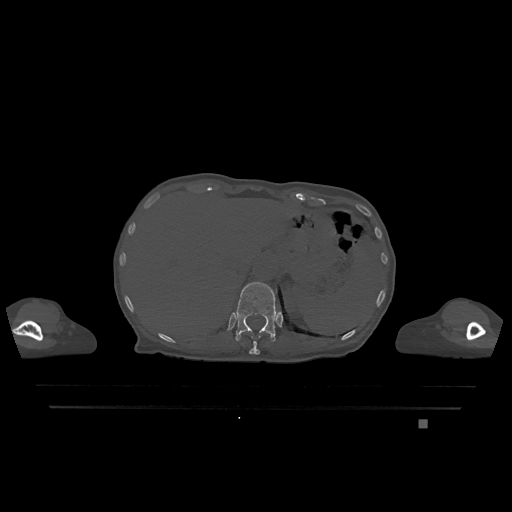
CT including the spine, one axial slice; slice 548 of 1317 in the series (ordered by position); bone window (W 1800 / L 400 HU); 0.5 mm slice thickness; 512 × 512 image matrix, field of view 500 × 500 mm. Female patient, age 74 years. From the clinical record (not read from this slice): primary cancer: lung.
Structures marked on this image (semi-automatic segmentation, software-assisted and operator-edited):
- T11 vertebra: bounding box [x1, y1, x2, y2] px = [249, 336, 261, 355]
- T12 vertebra: [236, 282, 278, 342]